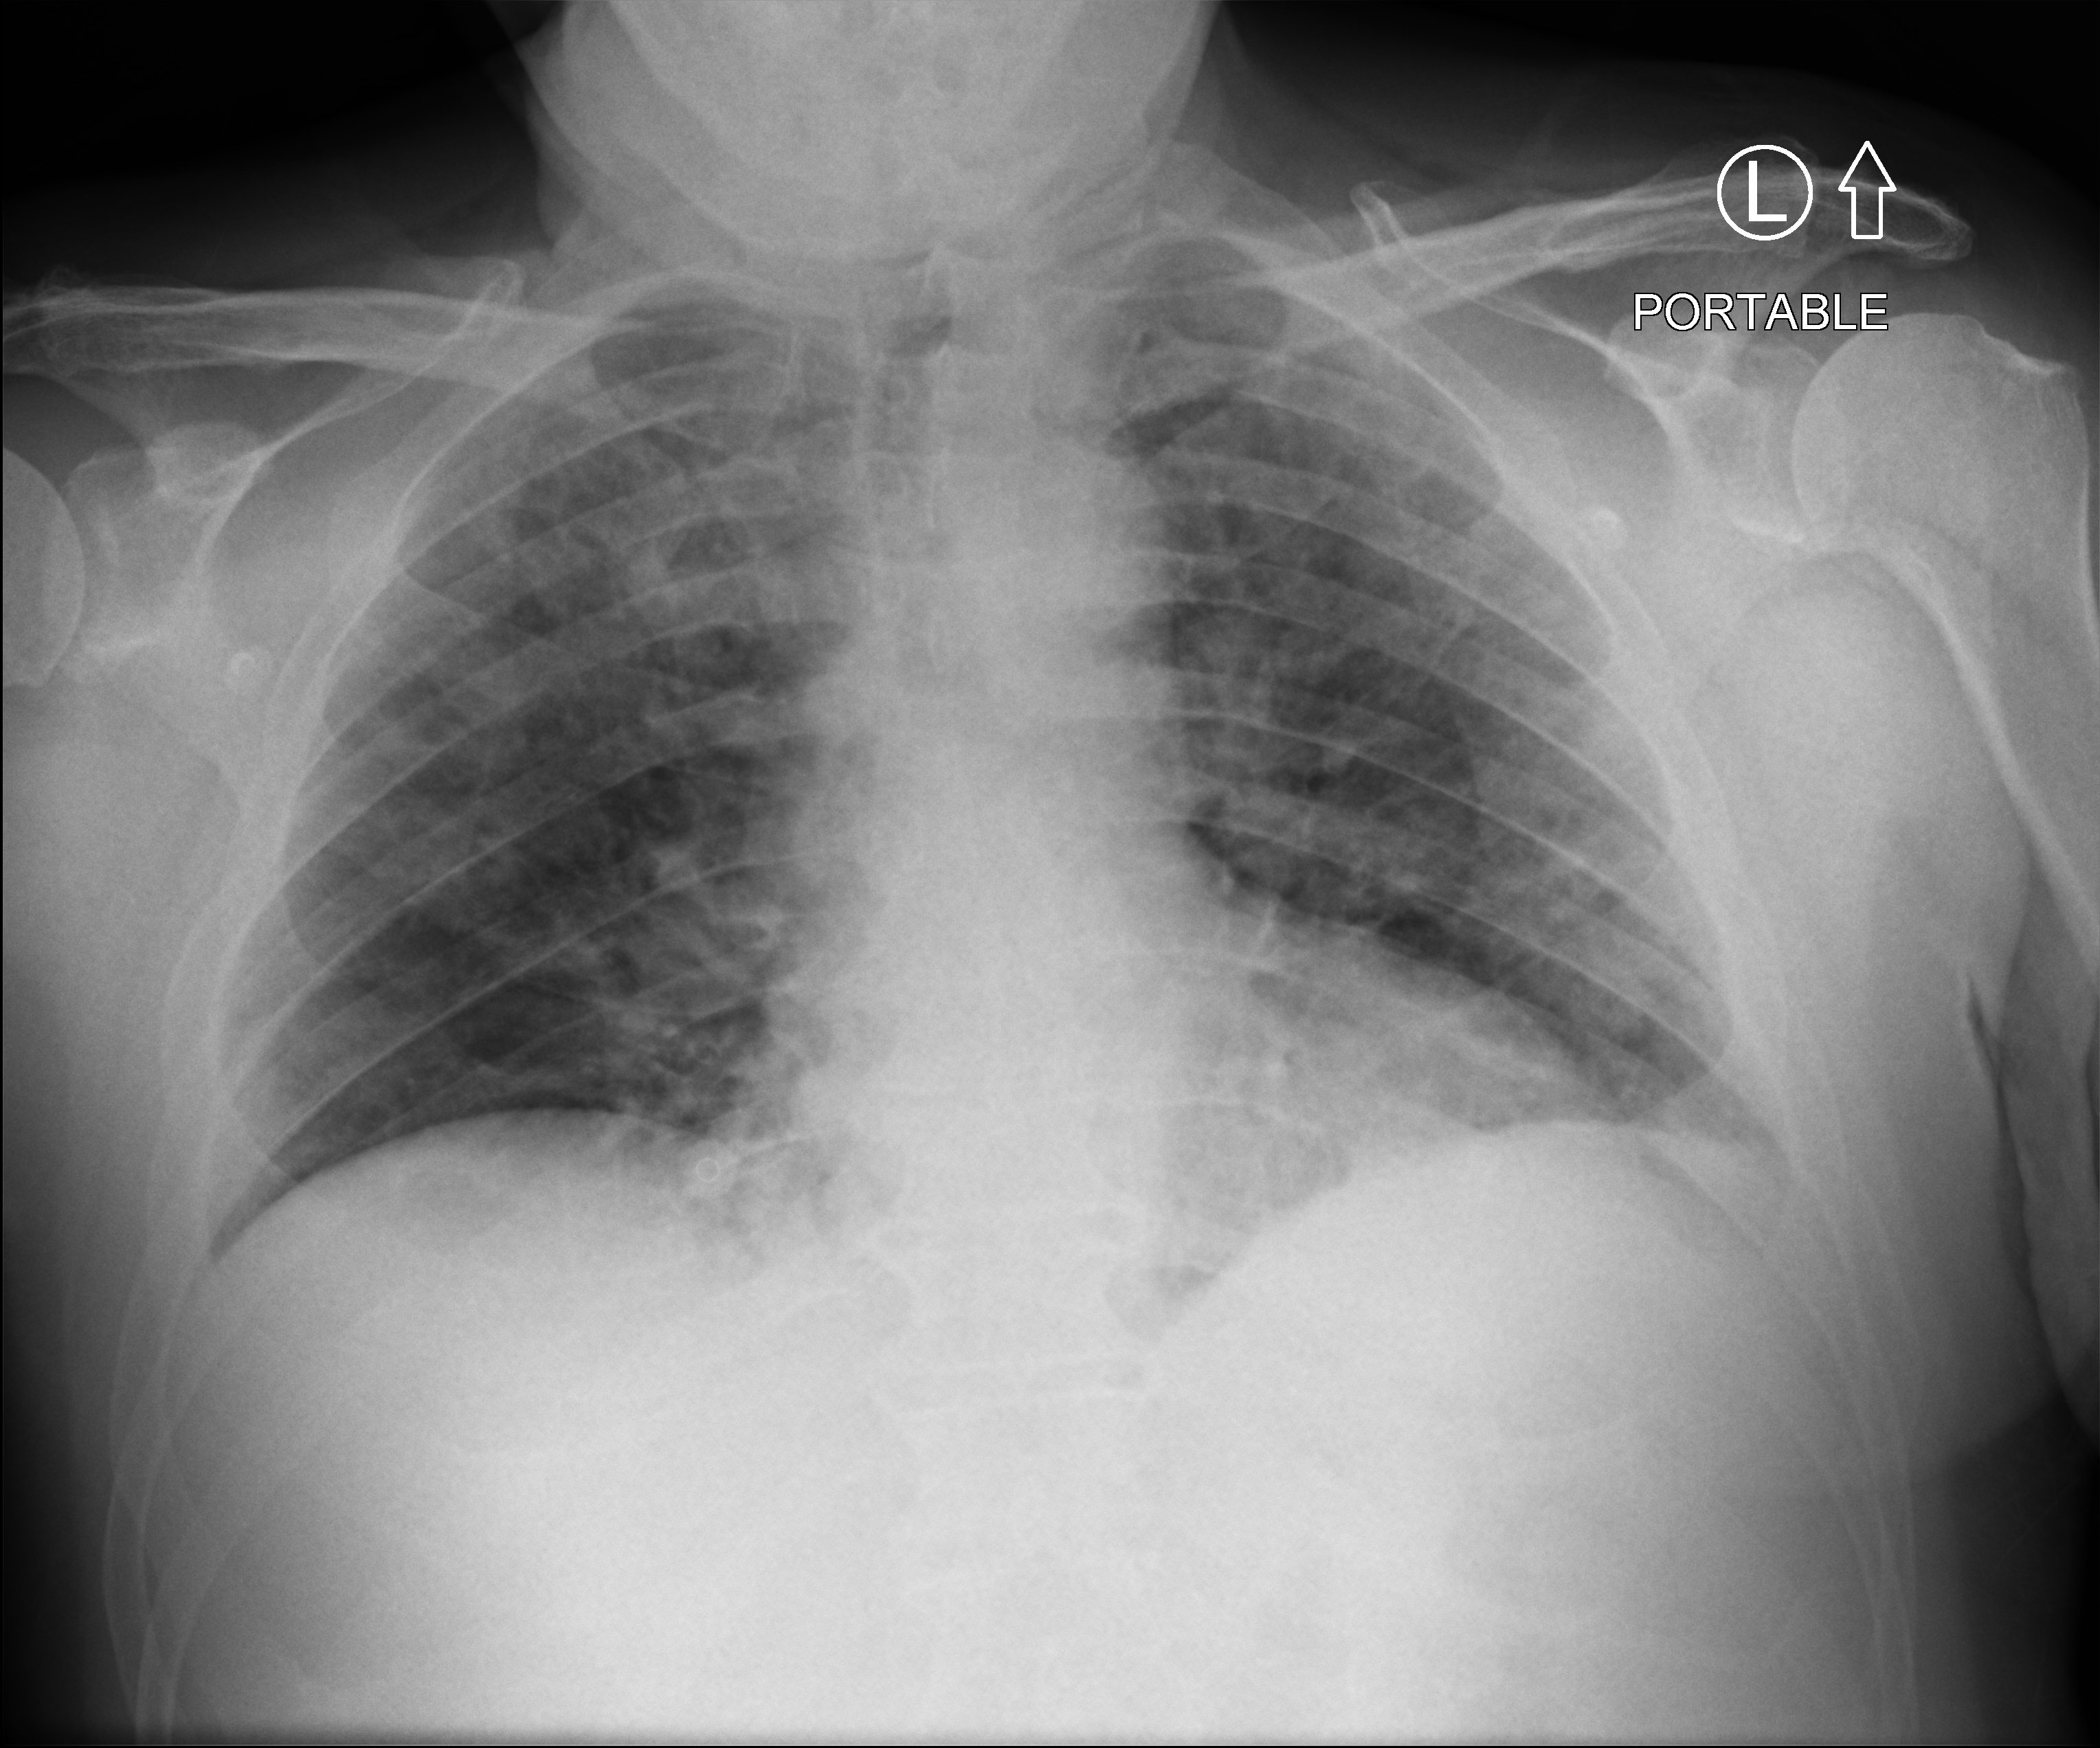
Portable chest radiograph, anteroposterior (AP) projection. Patient hospitalised with COVID-19; male, aged 60–74 years.
Hospital-stay facts (about this admission, not read from this image; timing relative to this image not recorded): diabetes (admission record): yes; mechanically ventilated during this hospital stay: no; admitted to intensive care during this hospital stay: no.